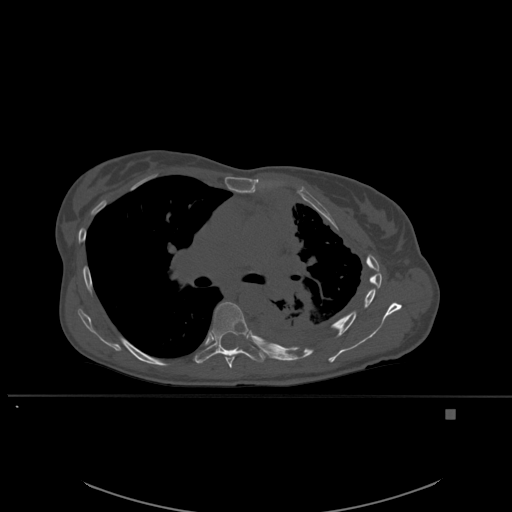
CT including the spine, one axial slice. Position 372 of 537 along the scan axis. Bone window (W 1800 / L 400 HU). 1.5 mm slice thickness. 512 × 512 image matrix, field of view 440 × 440 mm. Patient: female, 45 years. Case-level facts recorded for this patient, not image findings: primary cancer: lung.
Annotated regions visible in this slice (semi-automatically segmented with operator editing):
- T6 vertebra: bounding box [x1, y1, x2, y2] px = [225, 356, 235, 369]
- T7 vertebra: [196, 301, 267, 364]